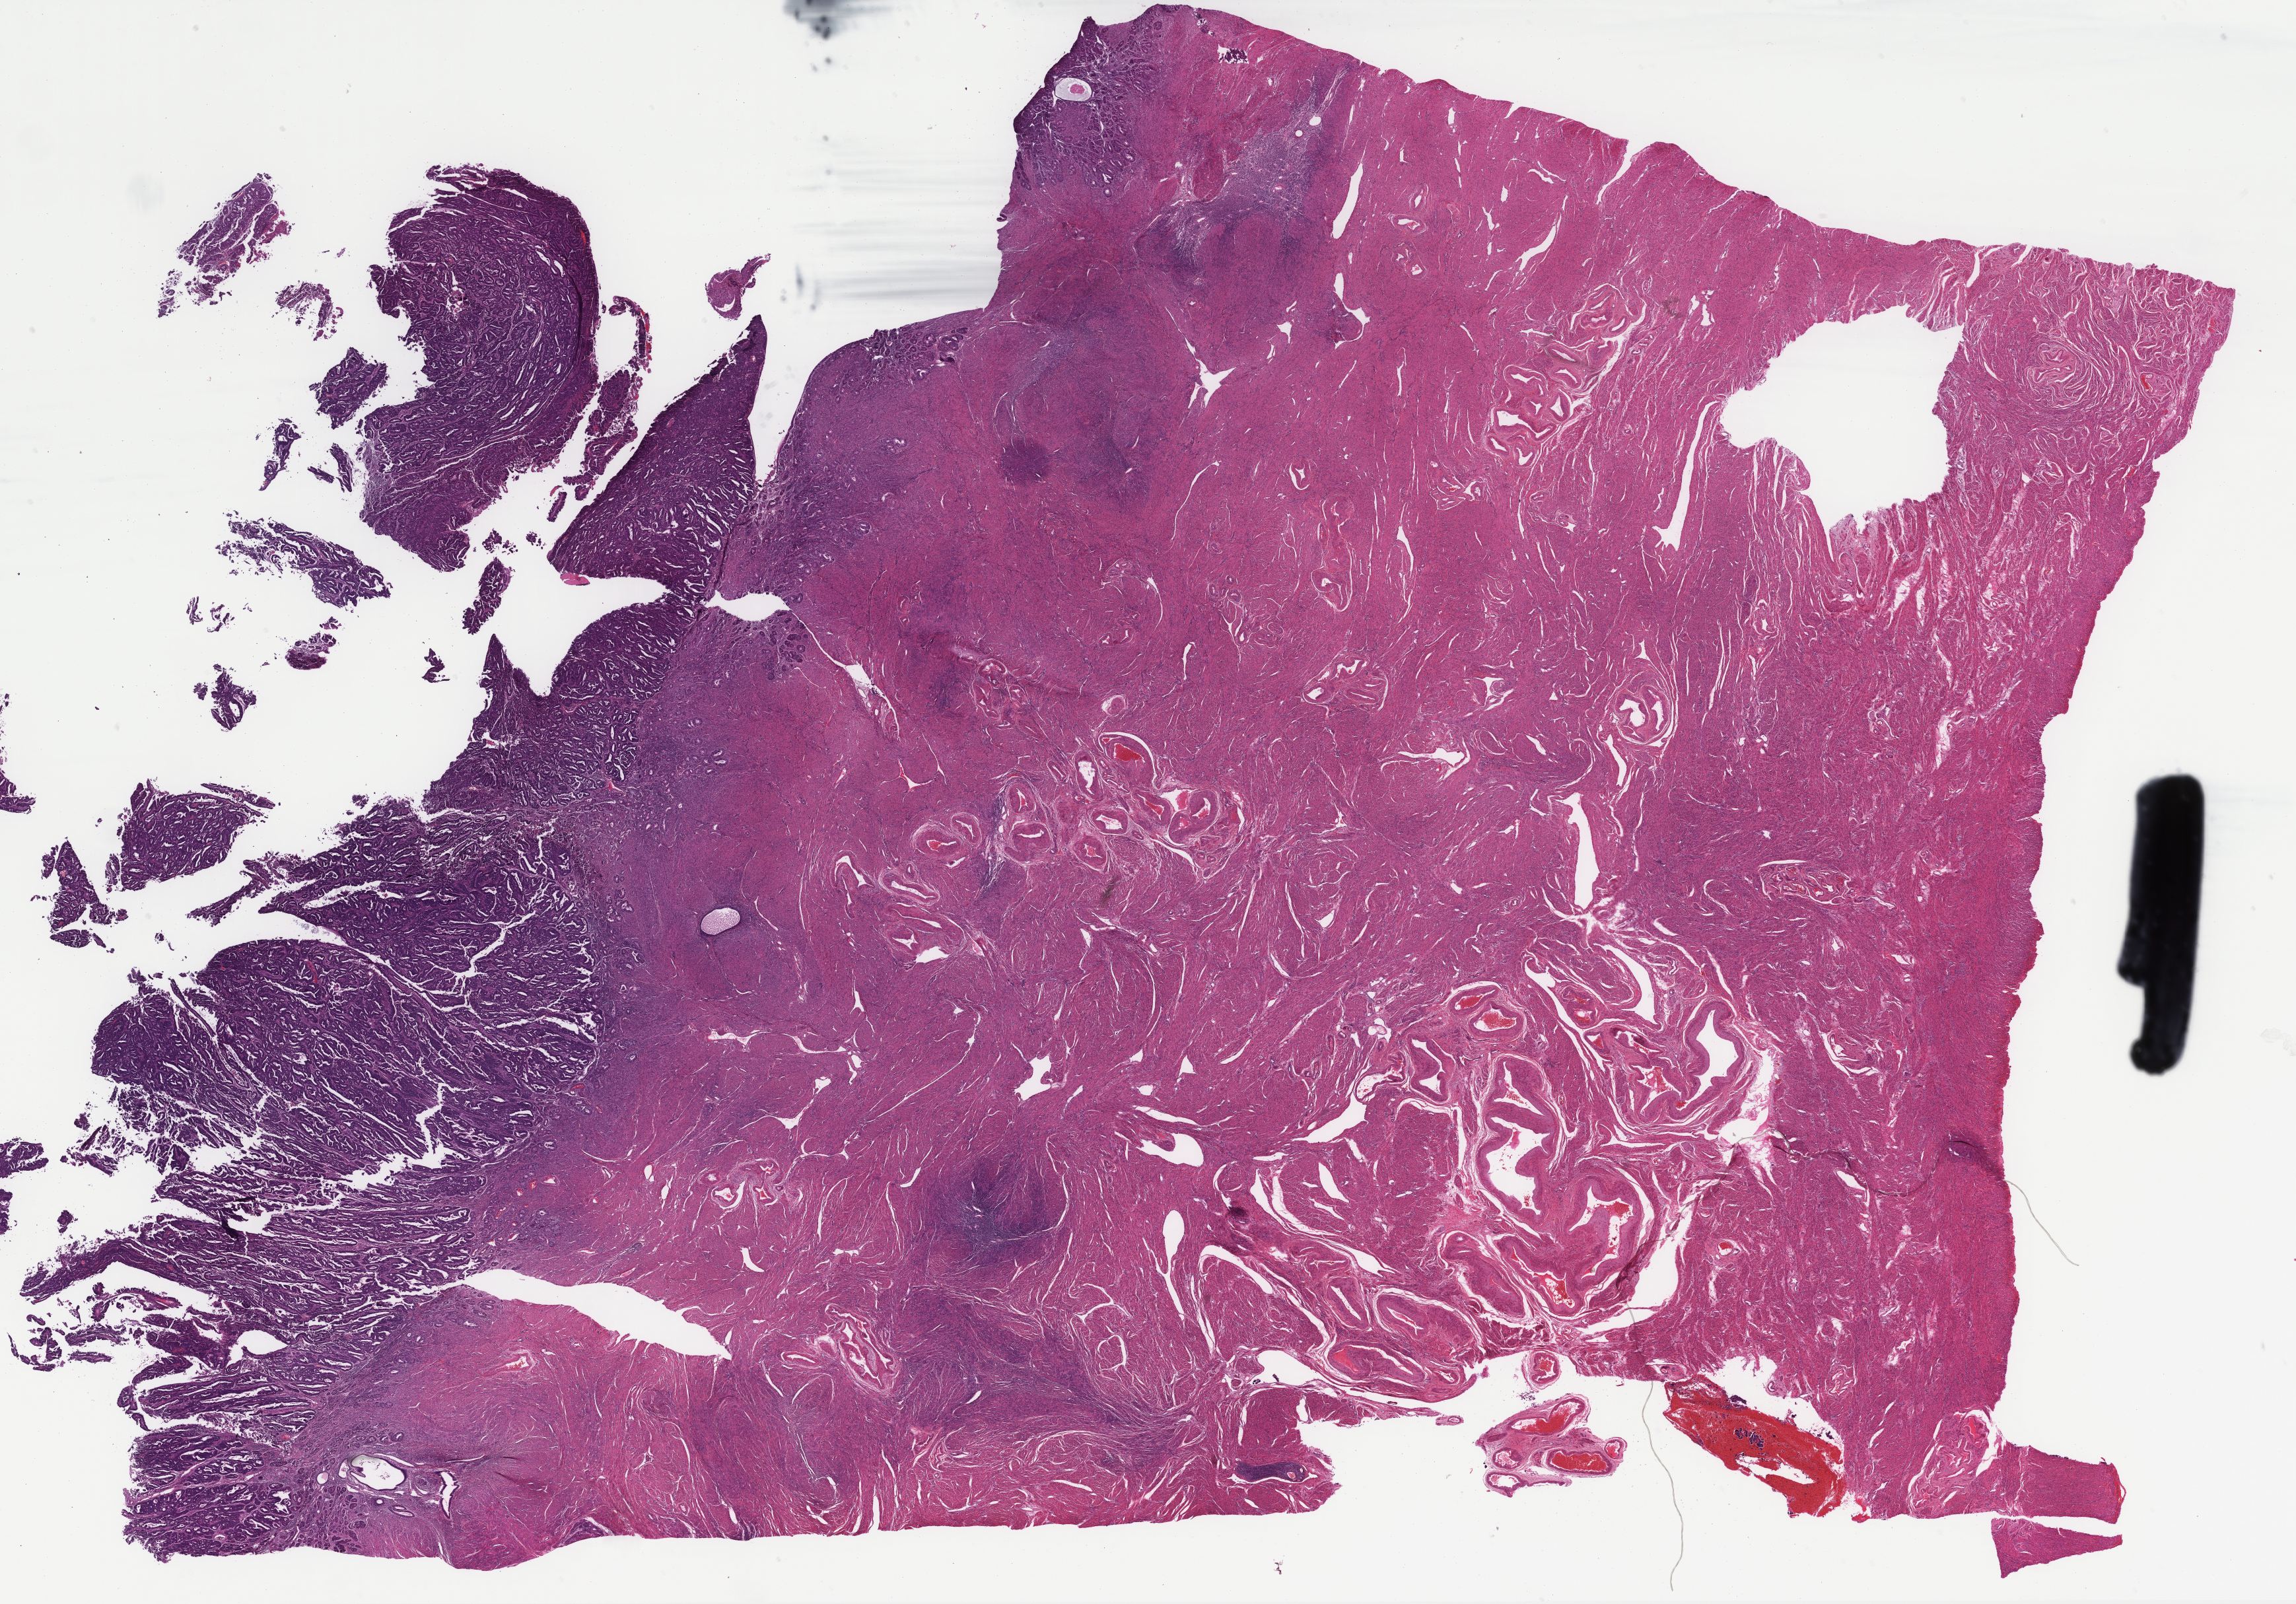
Hematoxylin and eosin (H&E) stained whole-slide image — whole scanned area (about 28.2 x 19.7 mm, acquisition: 40x scan) shown as a low-resolution overview. Formalin-fixed paraffin-embedded (FFPE) diagnostic section. Uterus, primary tumour sample. Female, age 71 years at initial diagnosis. Histologic grade: G3 (poorly differentiated).
Diagnosis: Endometrioid adenocarcinoma, NOS (endometrium). FIGO stage: IB.